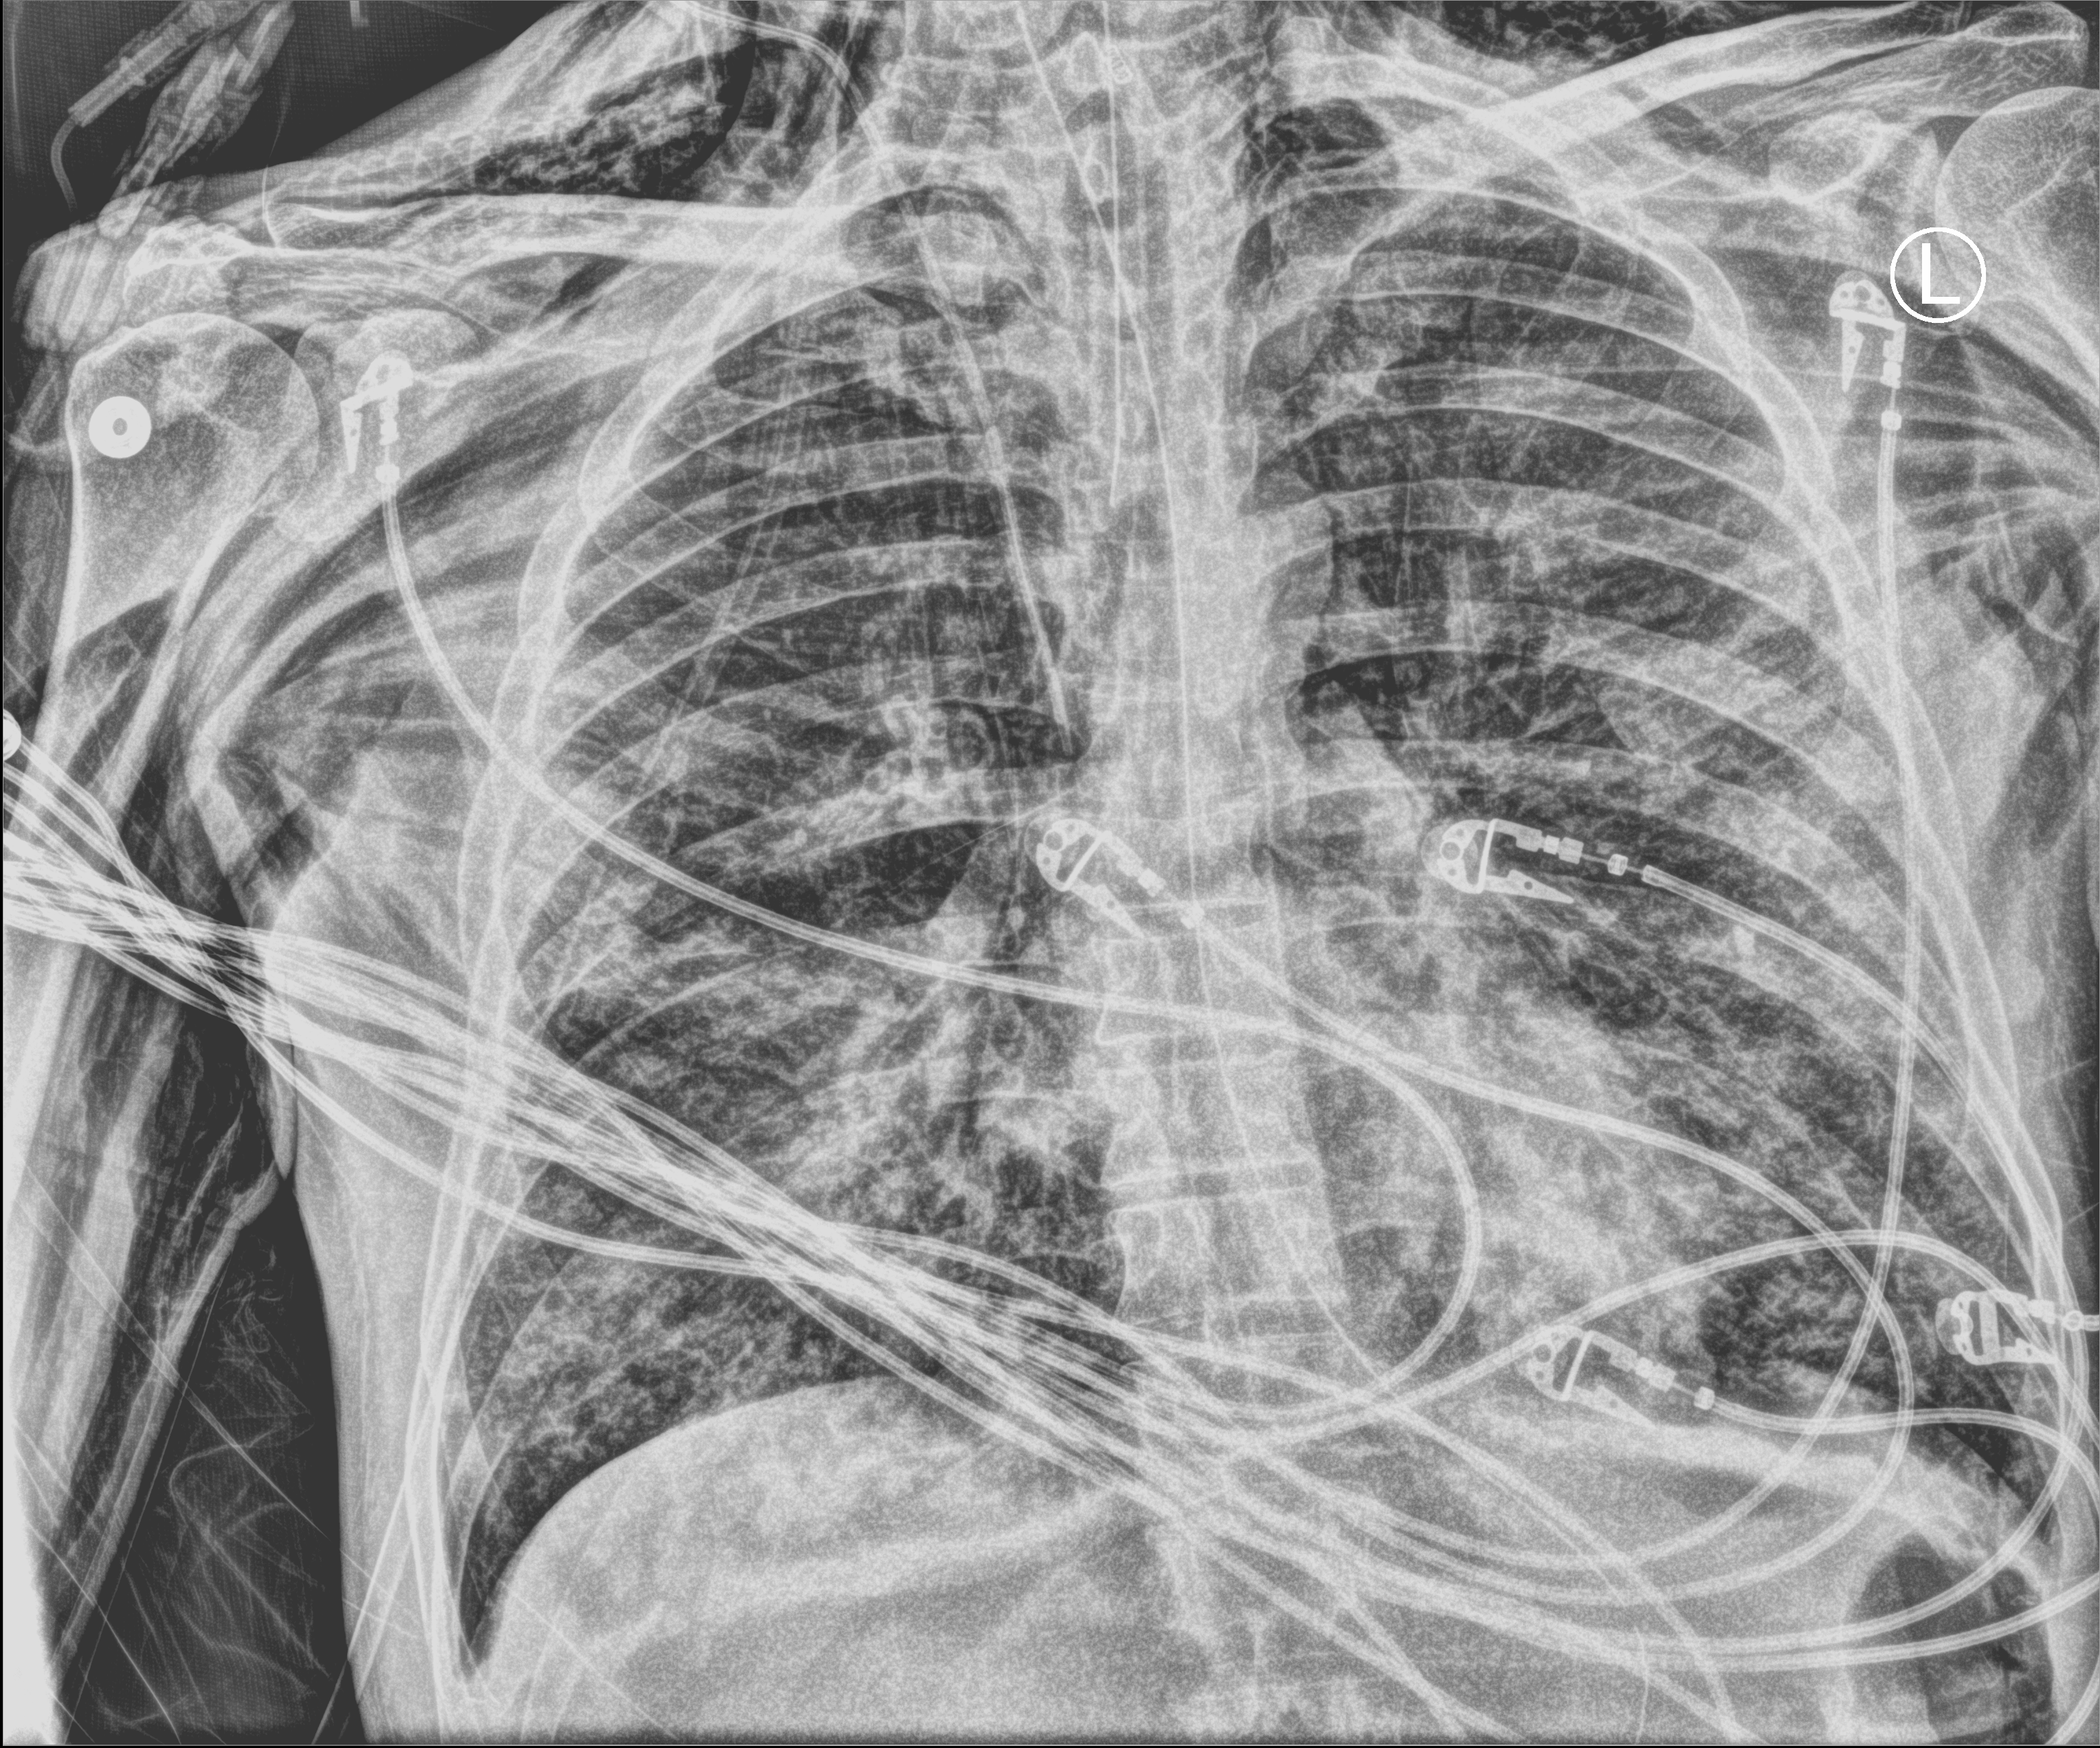
Chest X-ray (portable); anteroposterior (AP) projection. Patient hospitalised with COVID-19; male, aged 18–59 years.
From the hospital-stay record, not from the radiograph (when in the stay this image was taken is not recorded):
- COPD (admission record): no
- mechanically ventilated during this hospital stay: yes
- admitted to intensive care during this hospital stay: yes